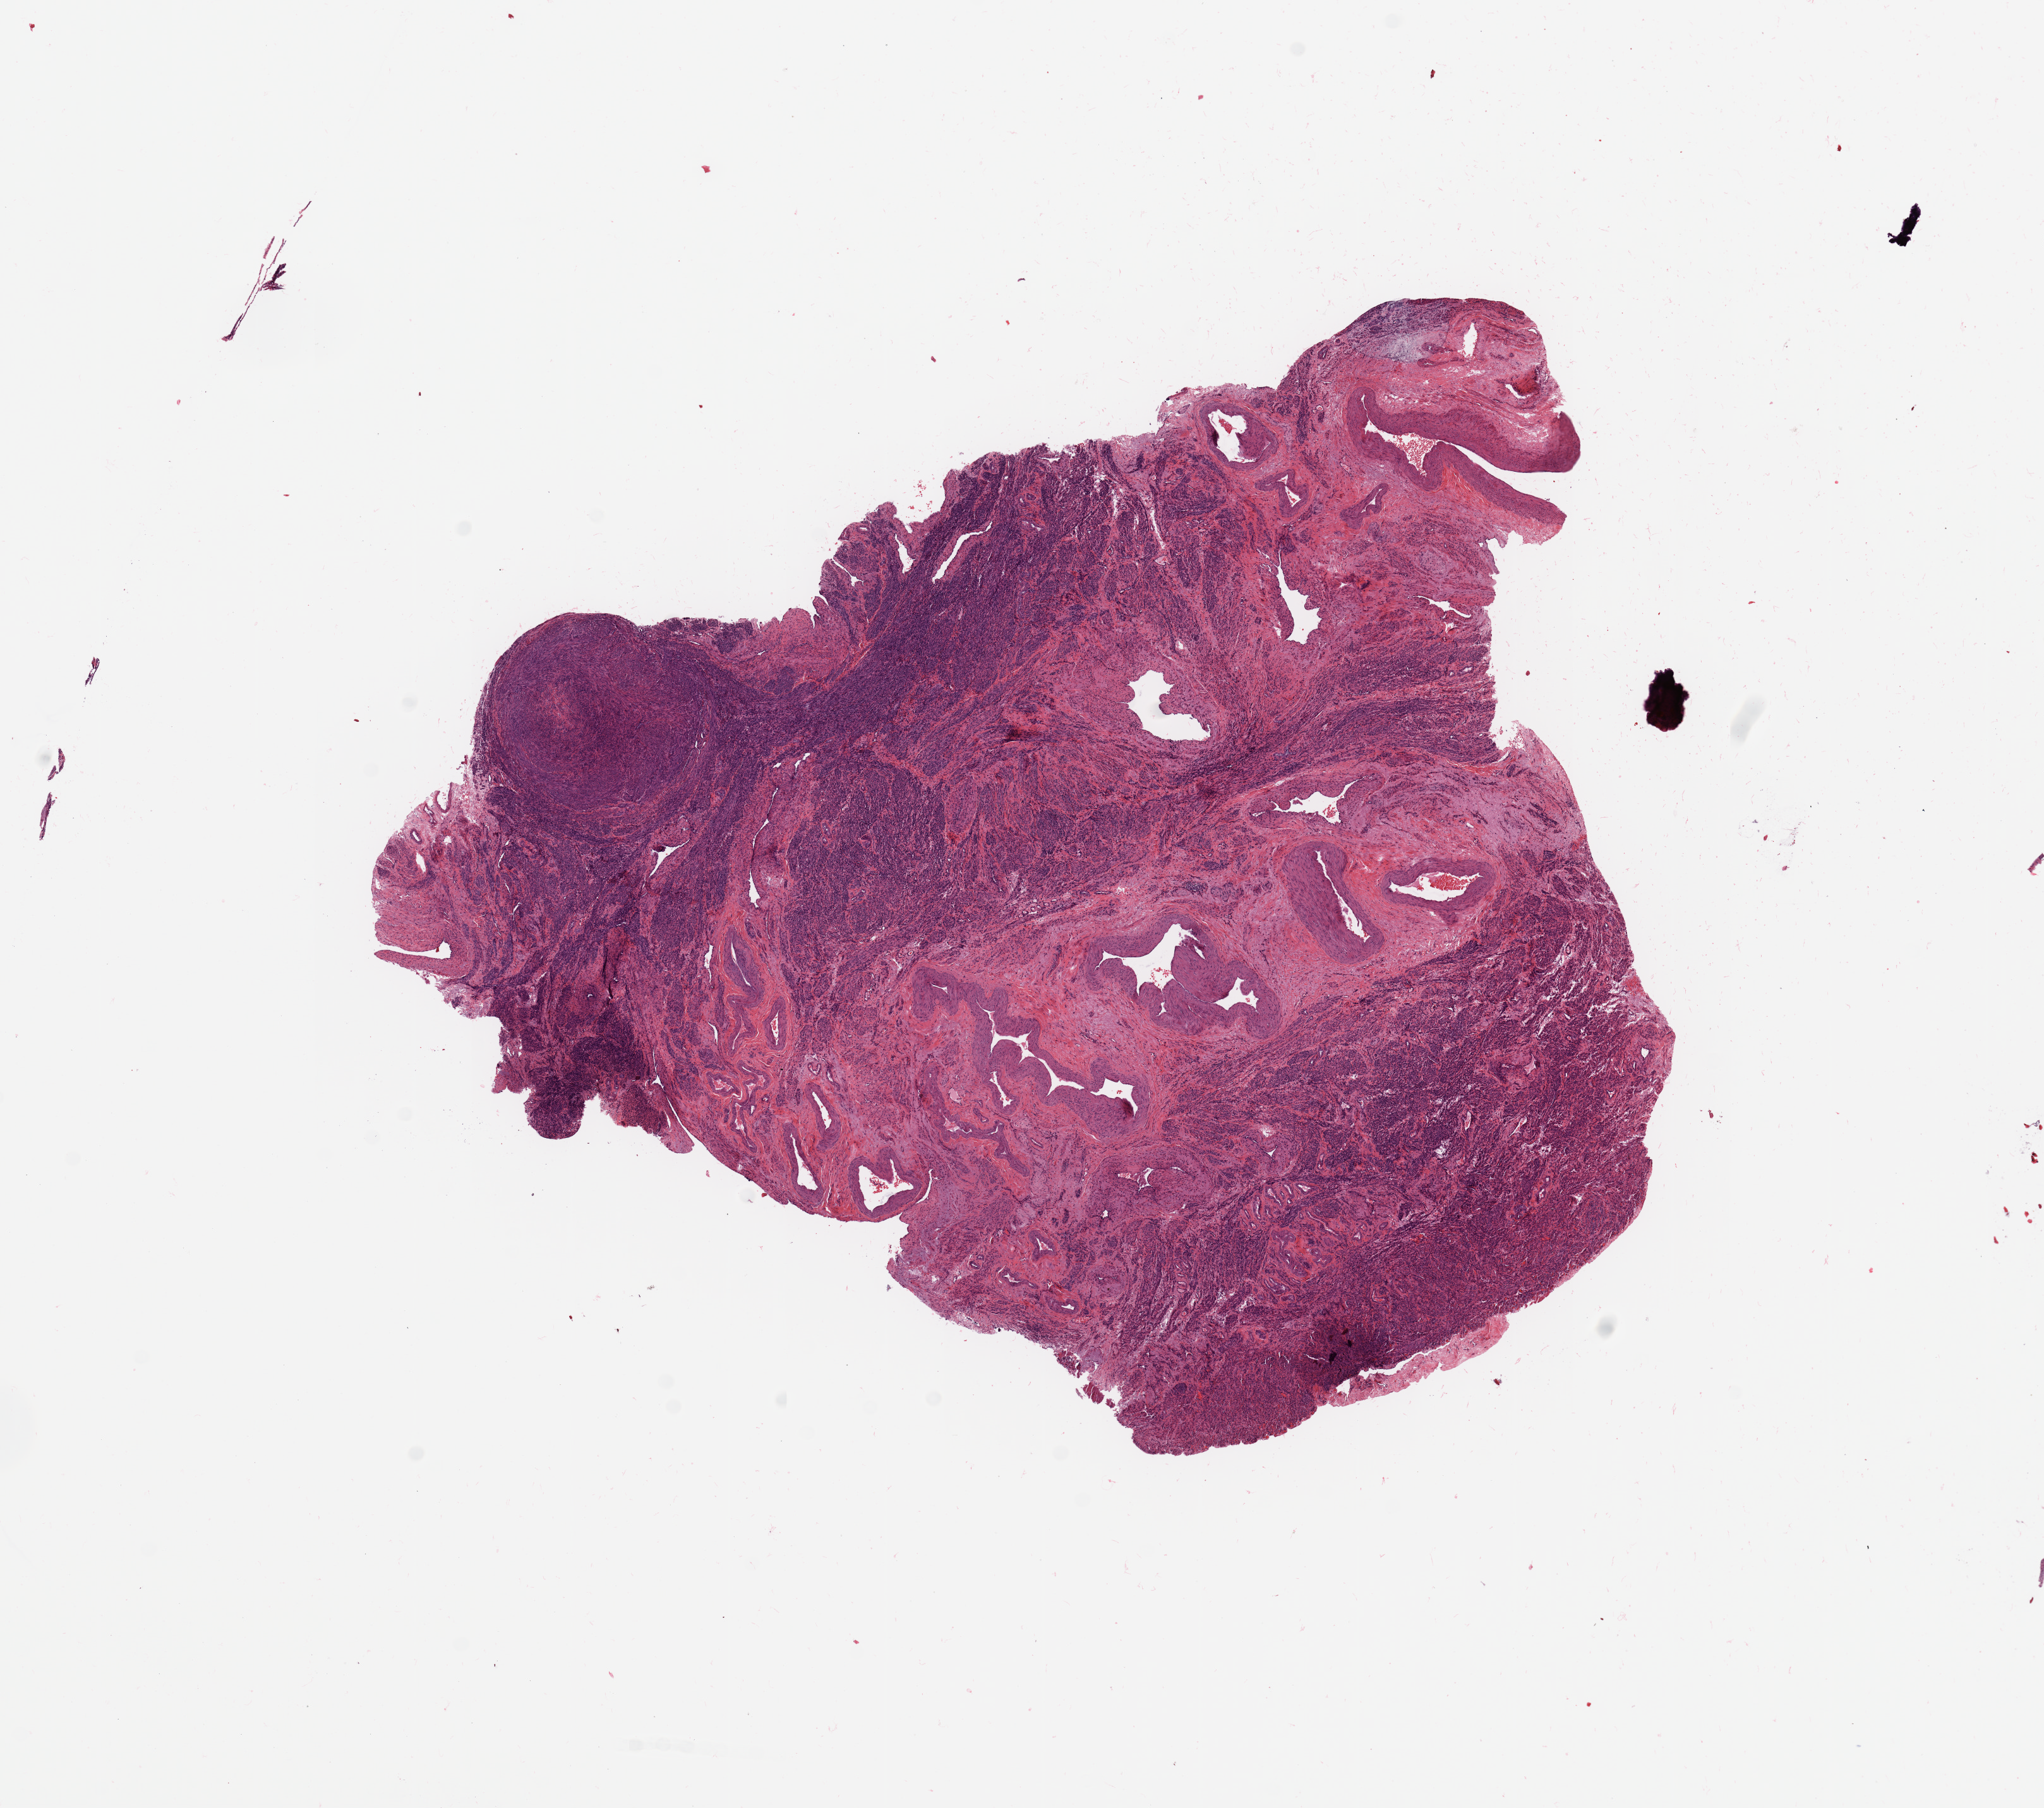
H&E-stained whole-slide image, low-resolution overview of the scanned area, about 12.8 x 11.3 mm (slide scanned at 20x), normal (non-tumour) tissue sample, uterus. 65-year-old female patient.
This section: normal (non-tumour) tissue from the same patient. Patient diagnosis: Endometrioid adenocarcinoma, NOS.